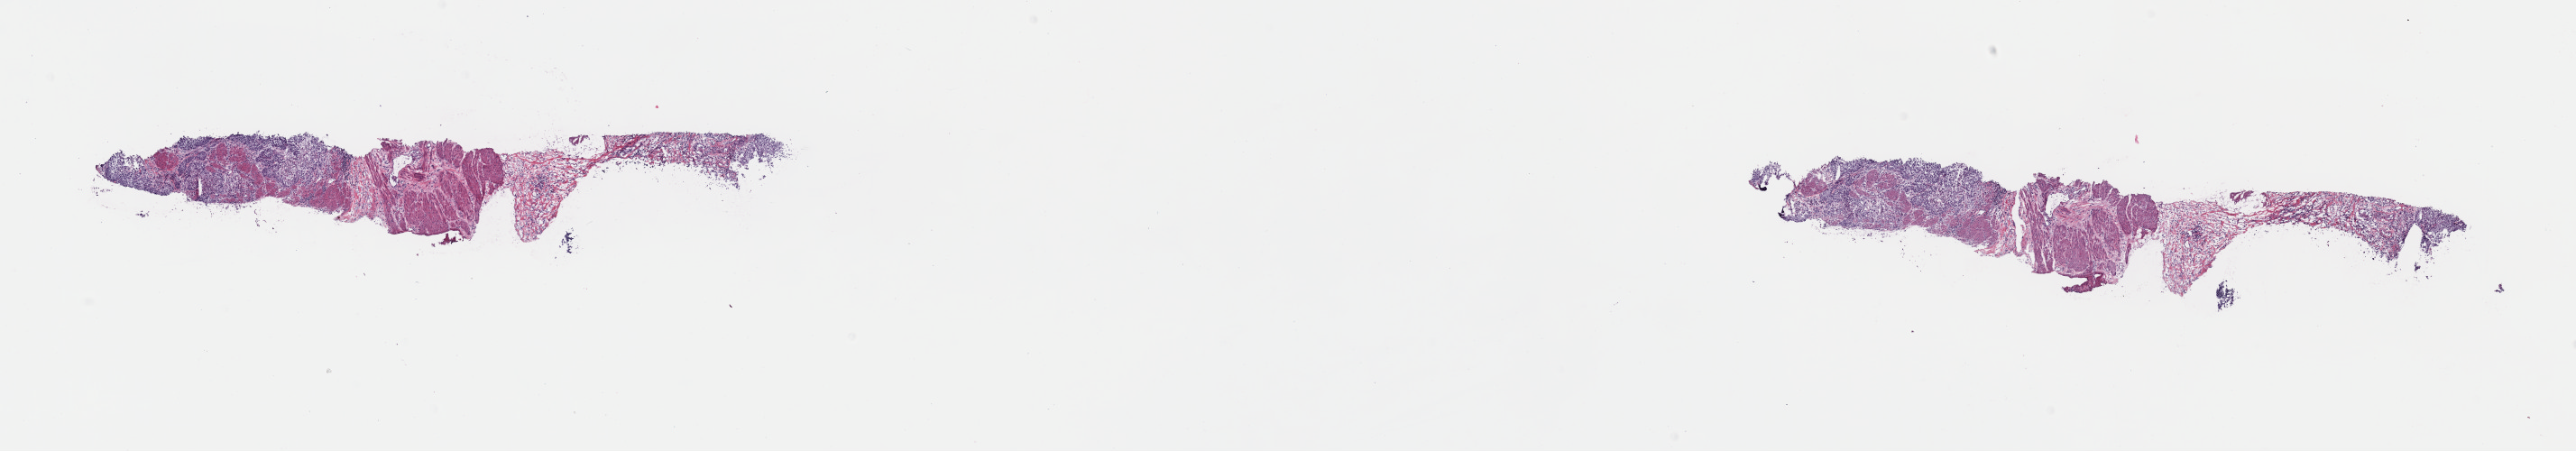
Whole-slide histology image, H&E, low-resolution overview of the scanned area, about 22.6 x 3.9 mm (slide scanned at 40x); frozen section; primary tumour sample from the bladder. Female, age 71 years at initial diagnosis. Histologic grade: high grade. Slide review estimates, as recorded: tumour cells 40%, tumour nuclei 60%, normal cells 60%, stromal cells 0%, necrosis 0%. Inflammatory infiltration, as recorded: lymphocyte infiltration 3%, monocyte infiltration 0%, neutrophil infiltration 0%.
AJCC pathologic stage: III (7th edition). Lymph nodes positive (case pathology): 0 of 26 examined. Pathologic diagnosis: Transitional cell carcinoma.